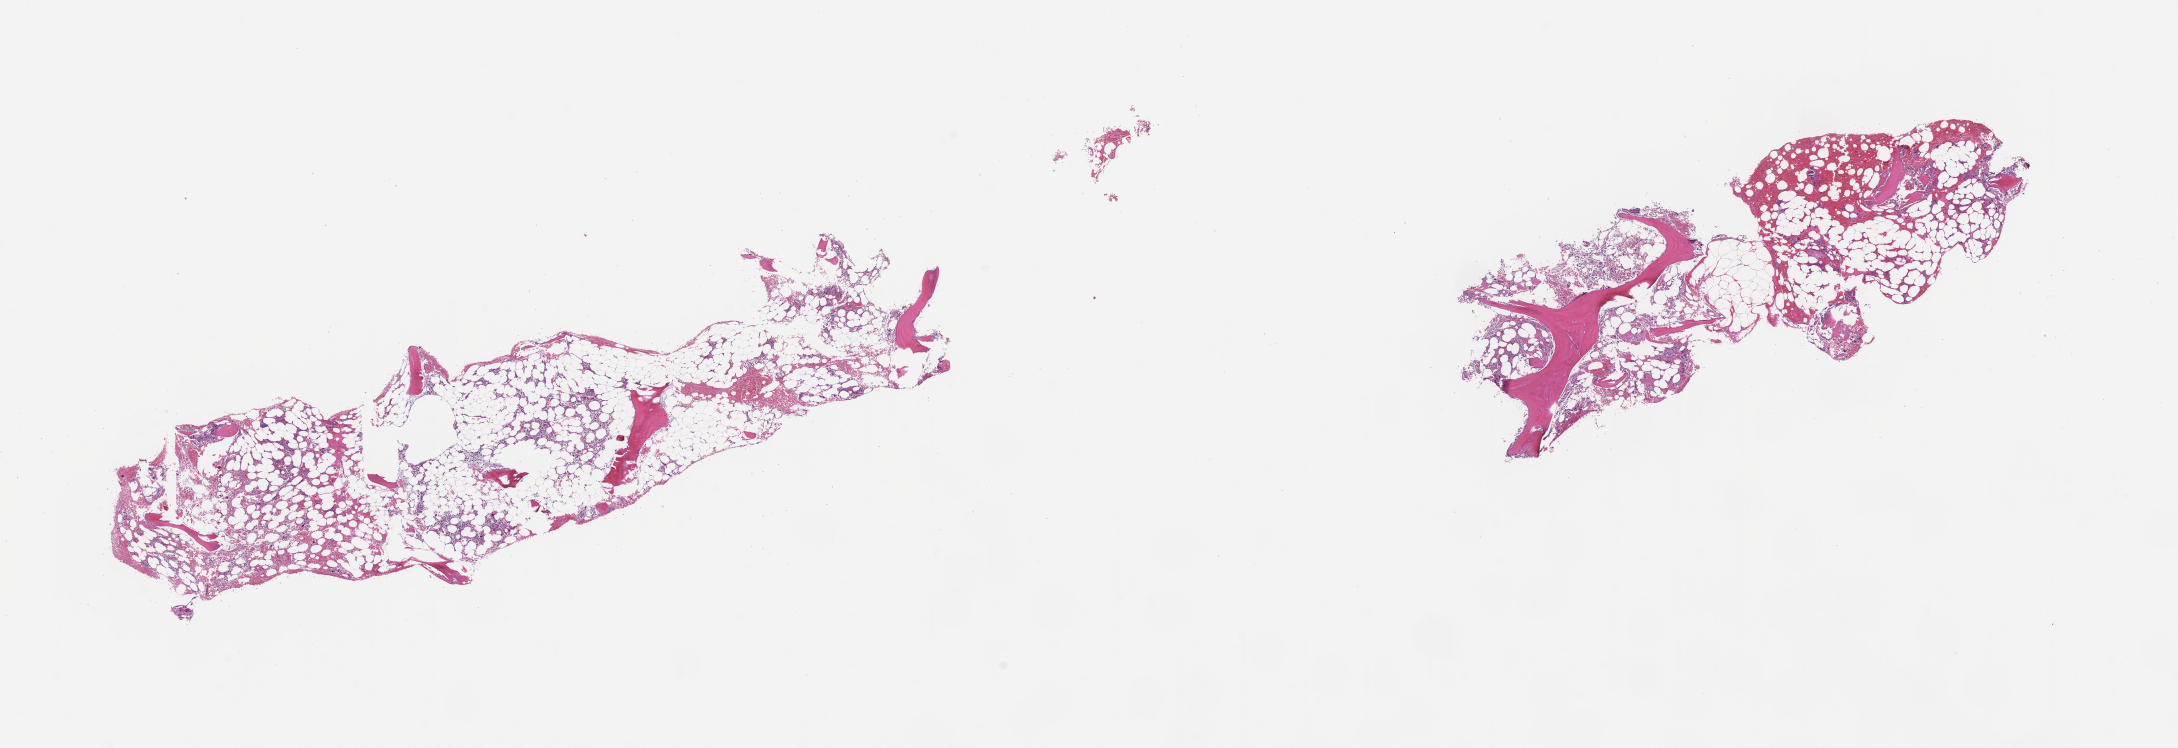
Whole-slide image, H&E stain — whole scanned area (about 17.6 x 6.0 mm) shown as a low-resolution overview. FFPE section. Site: bone marrow. Specimen time point: collected at baseline (before treatment). Patient: male.
* this section: primary tumour tissue
* diagnosis: Plasma Cell Myeloma